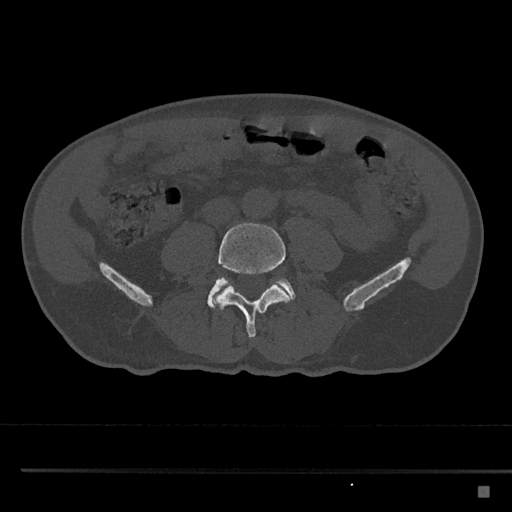
CT including the spine, one axial slice. Slice 623 of 797 in the series (ordered by position). Reconstruction kernel Br40s/3. 120 kVp. Bone window (W 1800 / L 400 HU). 512 × 512 image matrix, field of view 391 × 391 mm. Patient: male, 59 years. Case-level facts recorded for this patient, not image findings: primary cancer: prostate.
Structures marked on this image (semi-automatic segmentation, software-assisted and operator-edited):
- L4 vertebra: box from (x=214, y=223) to (x=290, y=338) px
- L5 vertebra: (x=207, y=277)–(x=296, y=309)